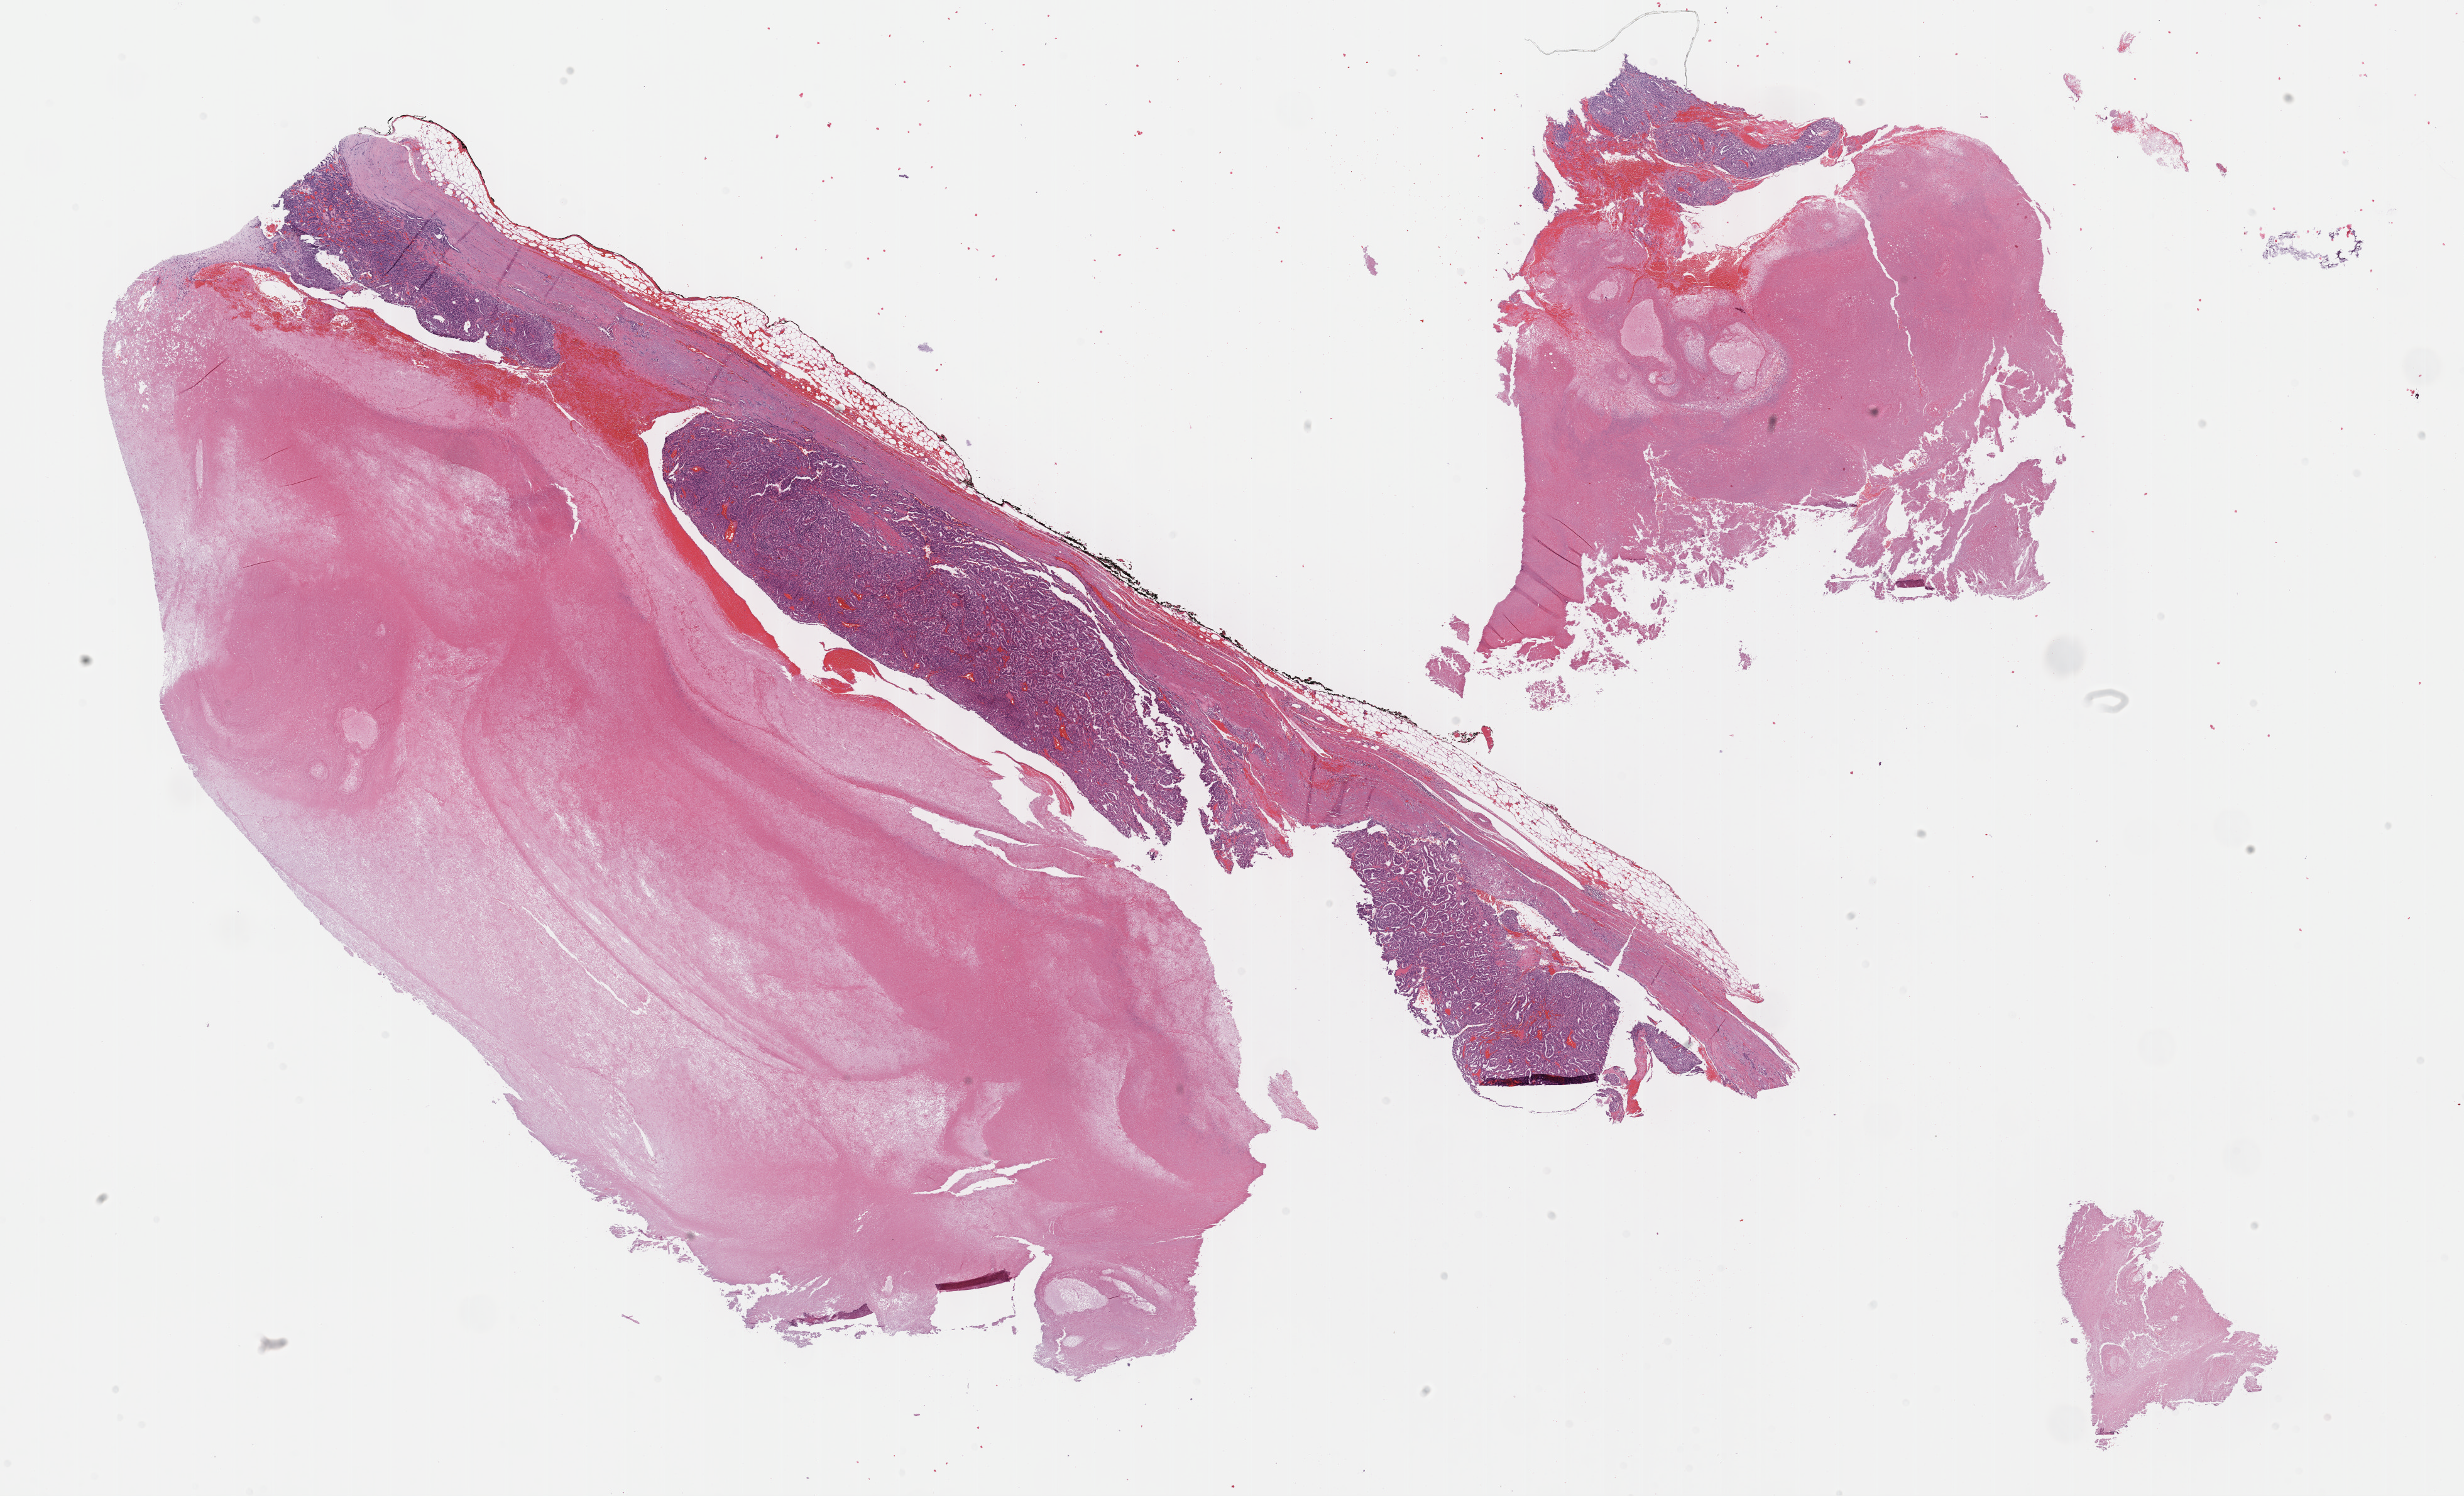
Whole-slide histology image, H&E-stained, low-resolution overview of the scanned area, about 31.7 x 19.2 mm (from a 40x scan), formalin-fixed paraffin-embedded (FFPE) diagnostic section, sample: primary tumour, kidney. Male, age 70 years at initial diagnosis.
- diagnosis: Papillary adenocarcinoma, NOS
- TNM: T2a NX MX
- laterality: left
- AJCC pathologic stage: IV (7th edition)